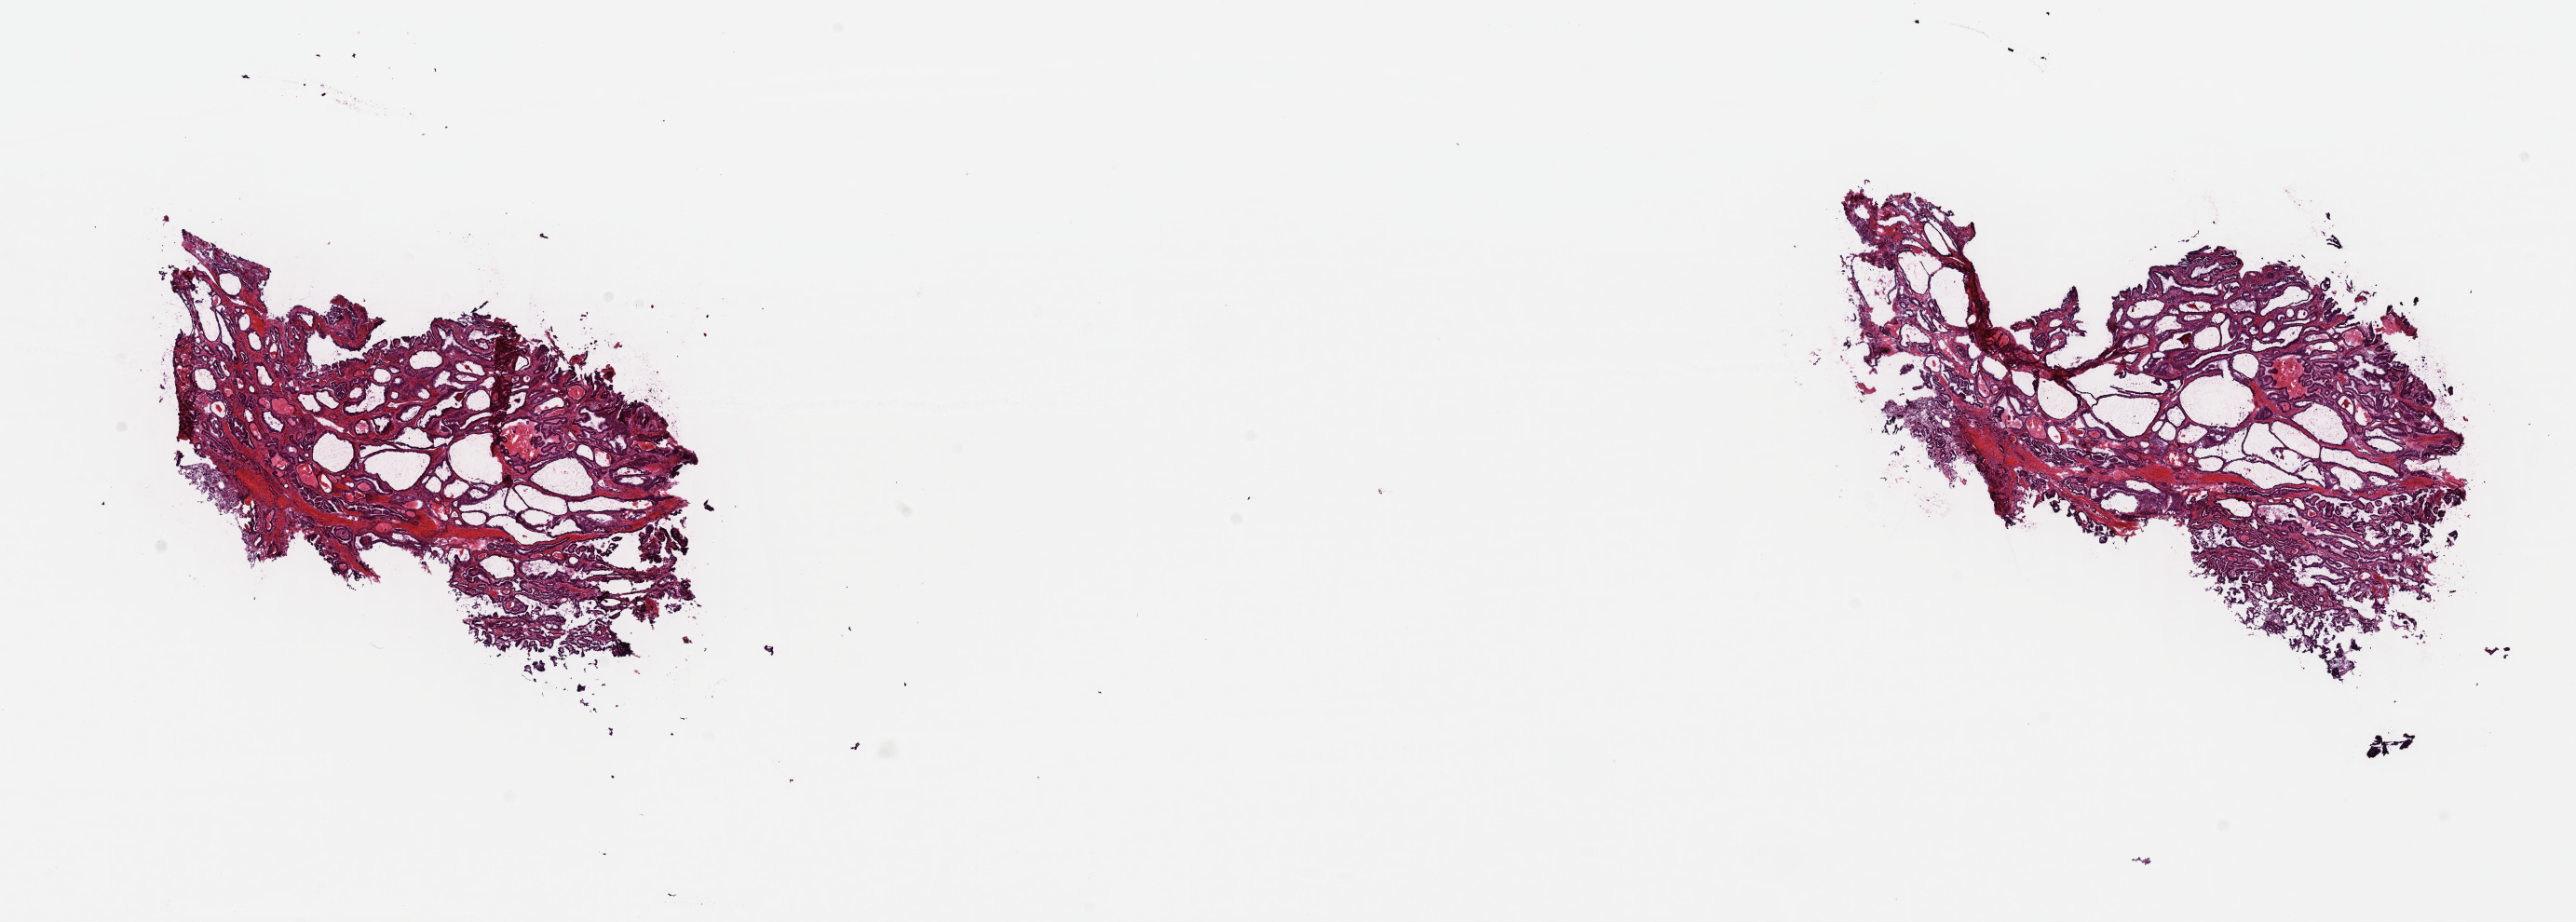
H&E whole-slide image — low-resolution overview of the scanned area, about 21.8 x 7.8 mm. Frozen section from the top of the tissue portion. Thyroid, primary tumour sample. Patient: female, age at initial diagnosis 63 years. Composition of this section per pathologist review: tumour cells 100%, tumour nuclei 70%, normal cells 0%, stromal cells 0%, necrosis 0%. Inflammatory infiltration, as recorded: lymphocyte infiltration 0%, monocyte infiltration 0%, neutrophil infiltration 0%.
- AJCC pathologic stage: II (7th edition)
- diagnosis: Papillary adenocarcinoma, NOS (thyroid gland)
- laterality: right